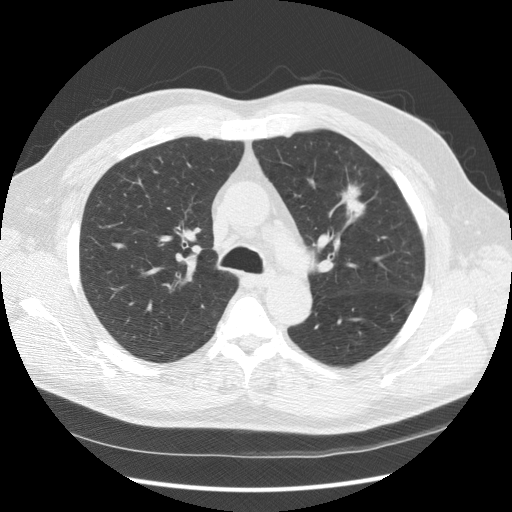
Axial slice from a low-dose chest CT screening exam, second screening round (one year after baseline), lung window (W 1500 / L -600 HU), standard (soft-tissue) reconstruction kernel (STANDARD), slice 53 of 157 in the series, 512 × 512 image matrix. Male, age 65 years at enrolment. Current smoker at enrolment.
Expert reader's lesion annotation, box from (x=325, y=171) to (x=378, y=231) px. The screening reader recorded 2 non-calcified nodules or masses ≥4 mm on this exam (left upper lobe, right upper lobe); which of them this box marks is not recorded. Official screen result: positive, other.